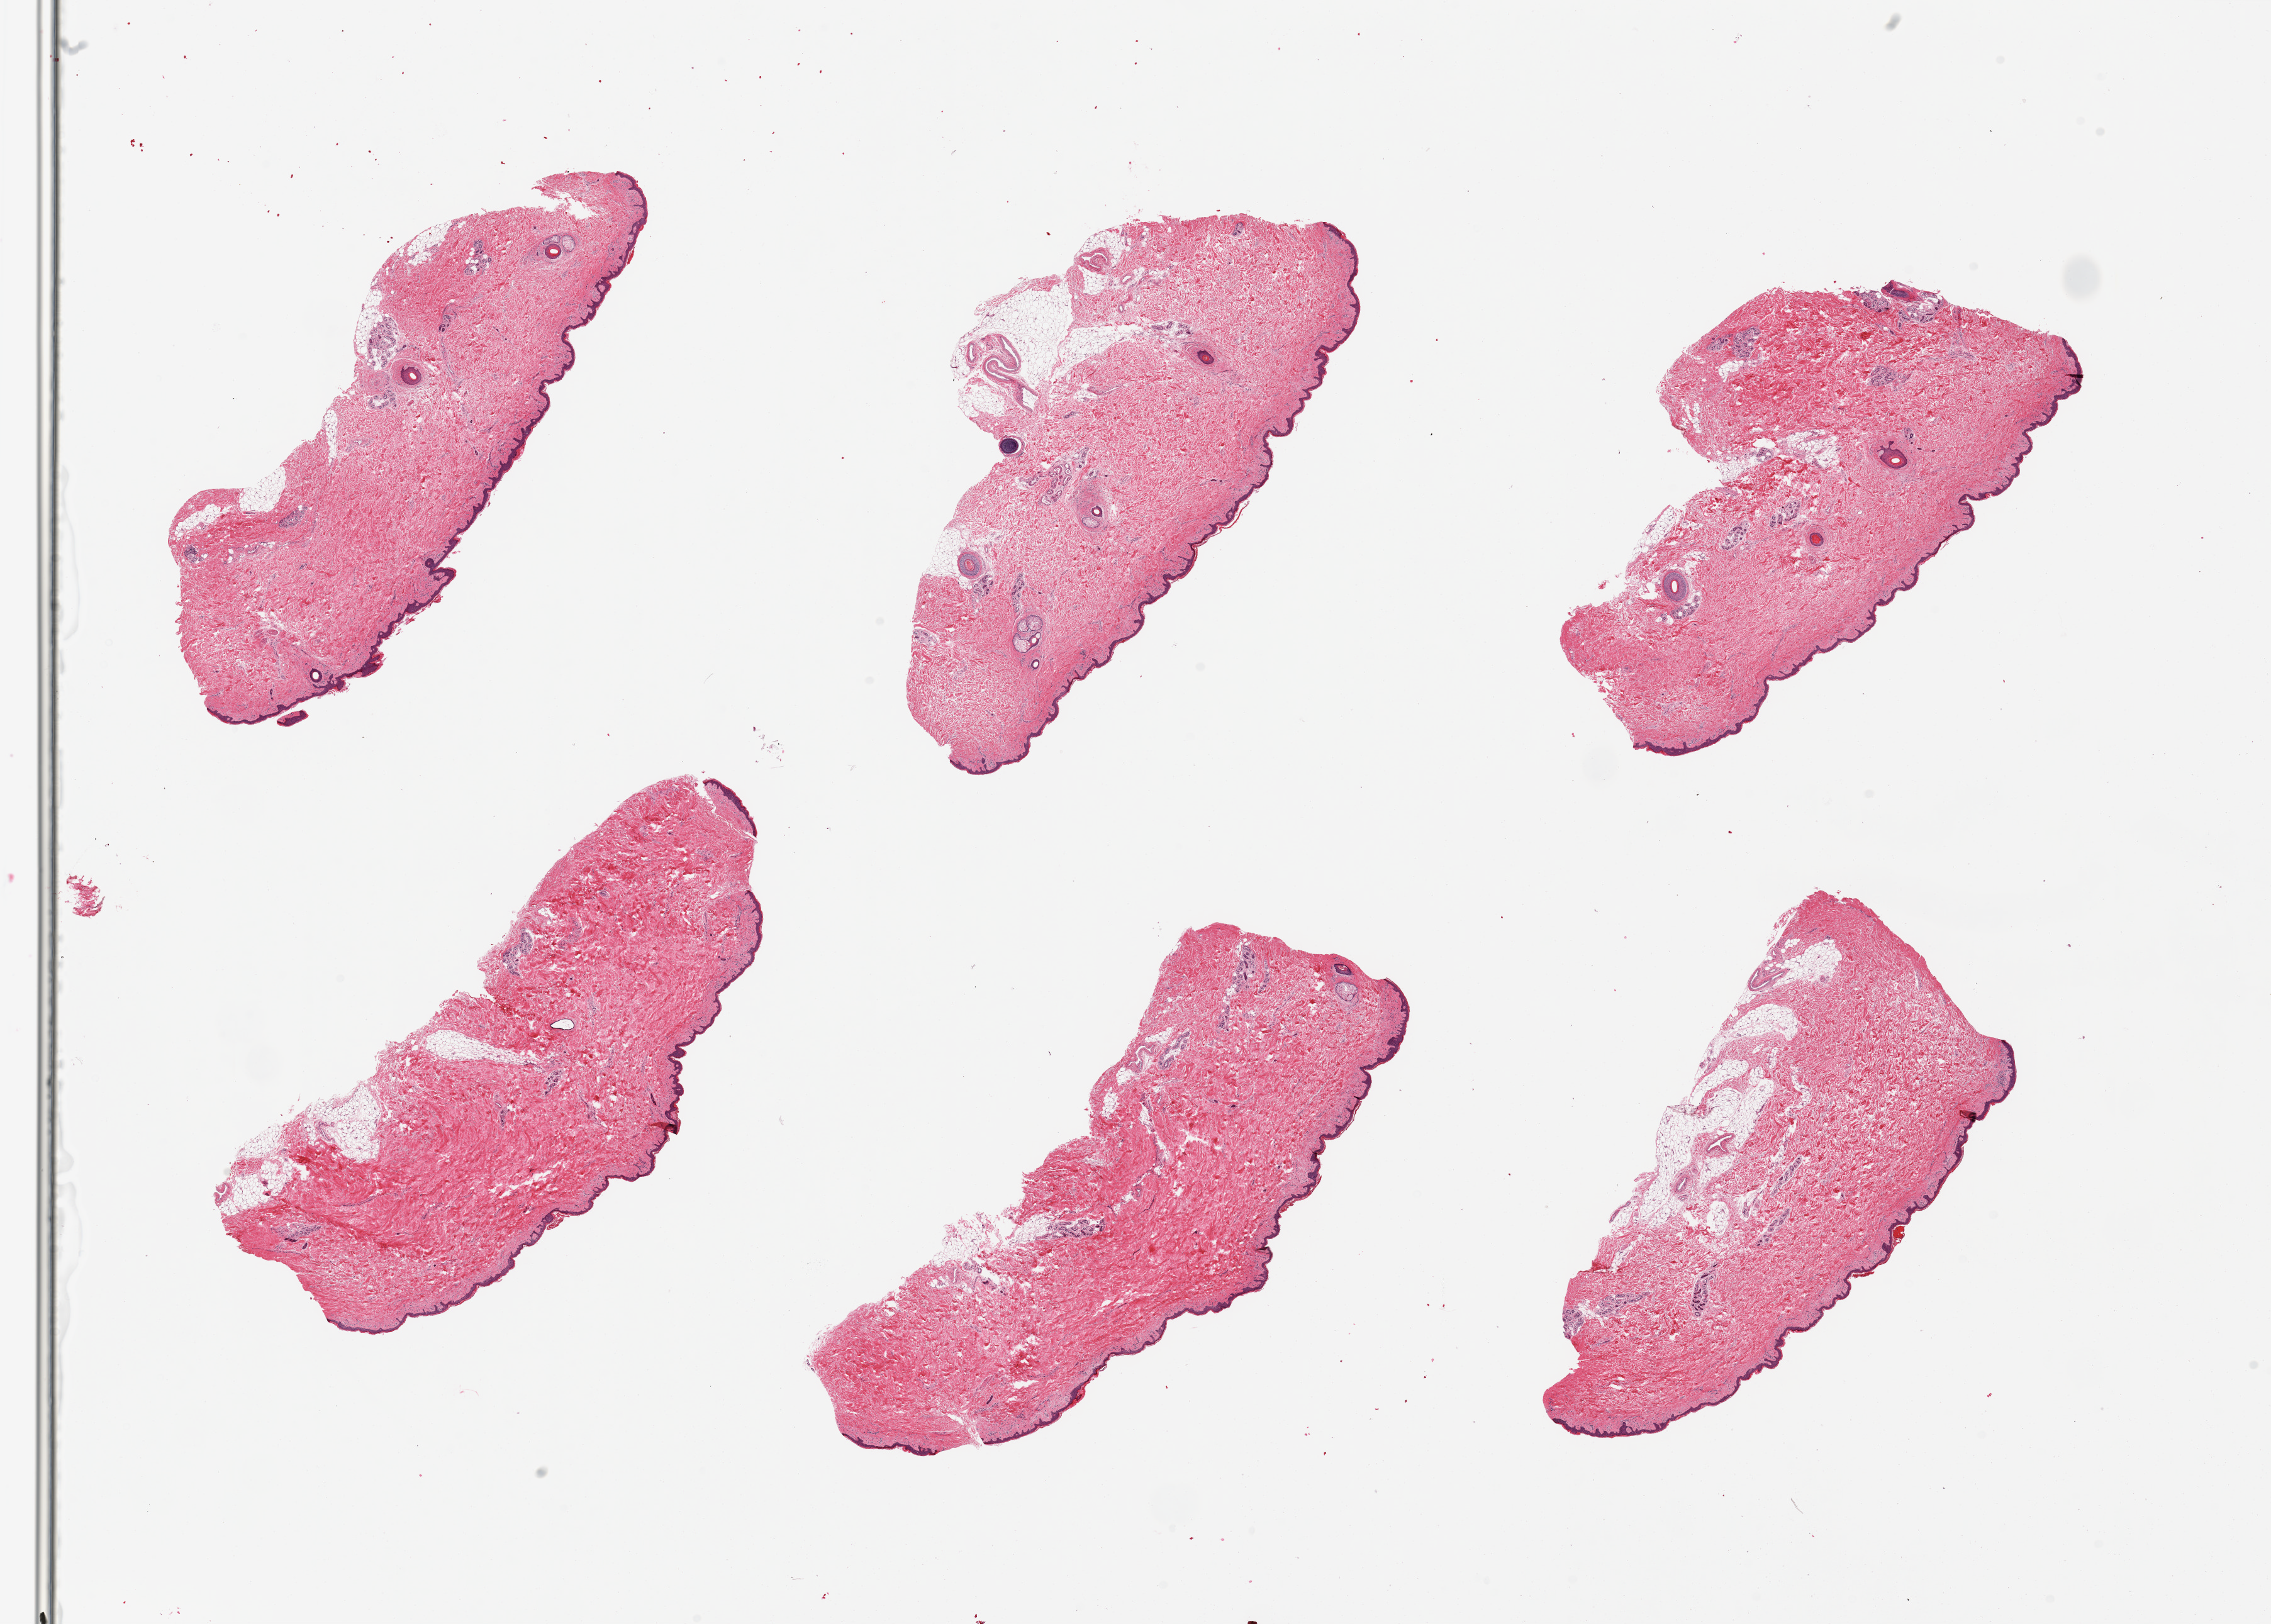
Whole-slide image, H&E stain, a low-resolution overview of the entire scanned area, about 28.5 x 20.4 mm (from a 20x scan); PAXgene-fixed, paraffin-embedded tissue; sampled site (target tissue): skin of suprapubic region; donor tissue sample. Male donor.
* reviewer comment on this tissue sample: 6 pieces; Squamous epithelium is ~30-45mcirons thick; Adherent dermal fat present focally